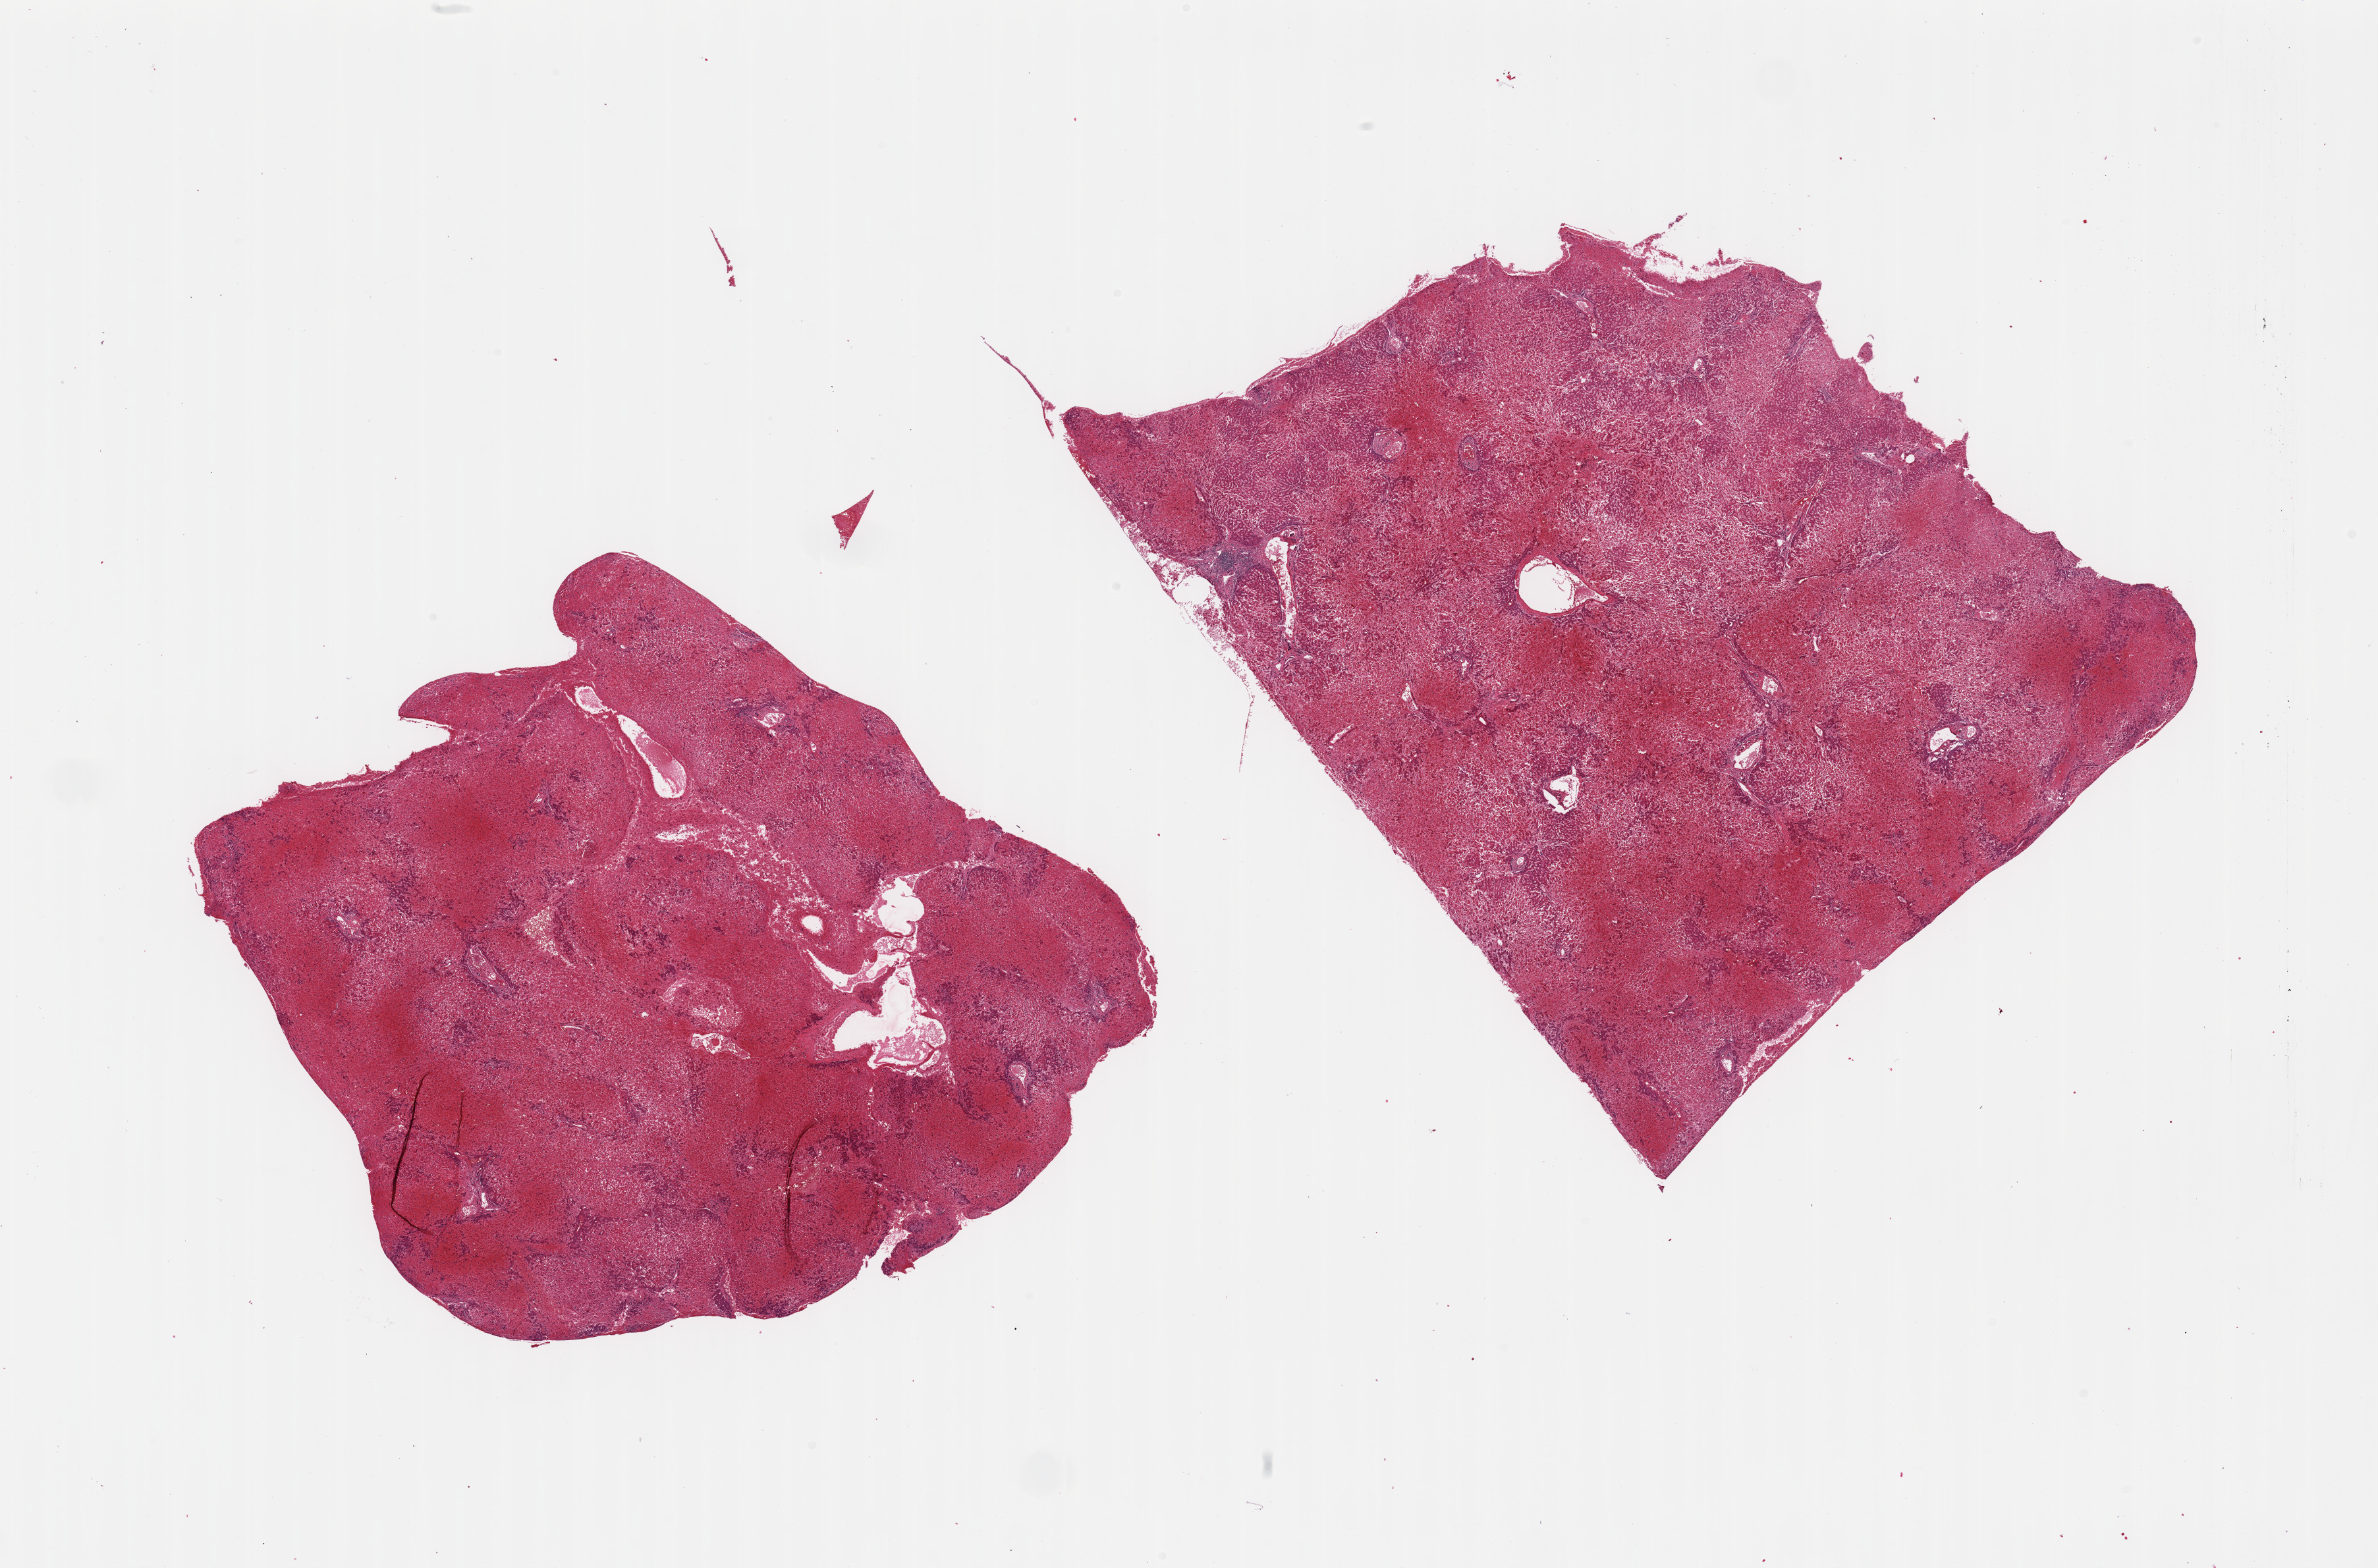
Haematoxylin and eosin whole-slide image — low-resolution overview of the scanned area, about 28.5 x 18.8 mm (from a 20x scan), PAXgene-fixed, paraffin-embedded tissue, section of liver (target tissue), tissue donor sample. Donor sex: male.
Pathologist's review note for this sample: 2 pieces; severe central lobular vascular congestion and liver cell necrosis.